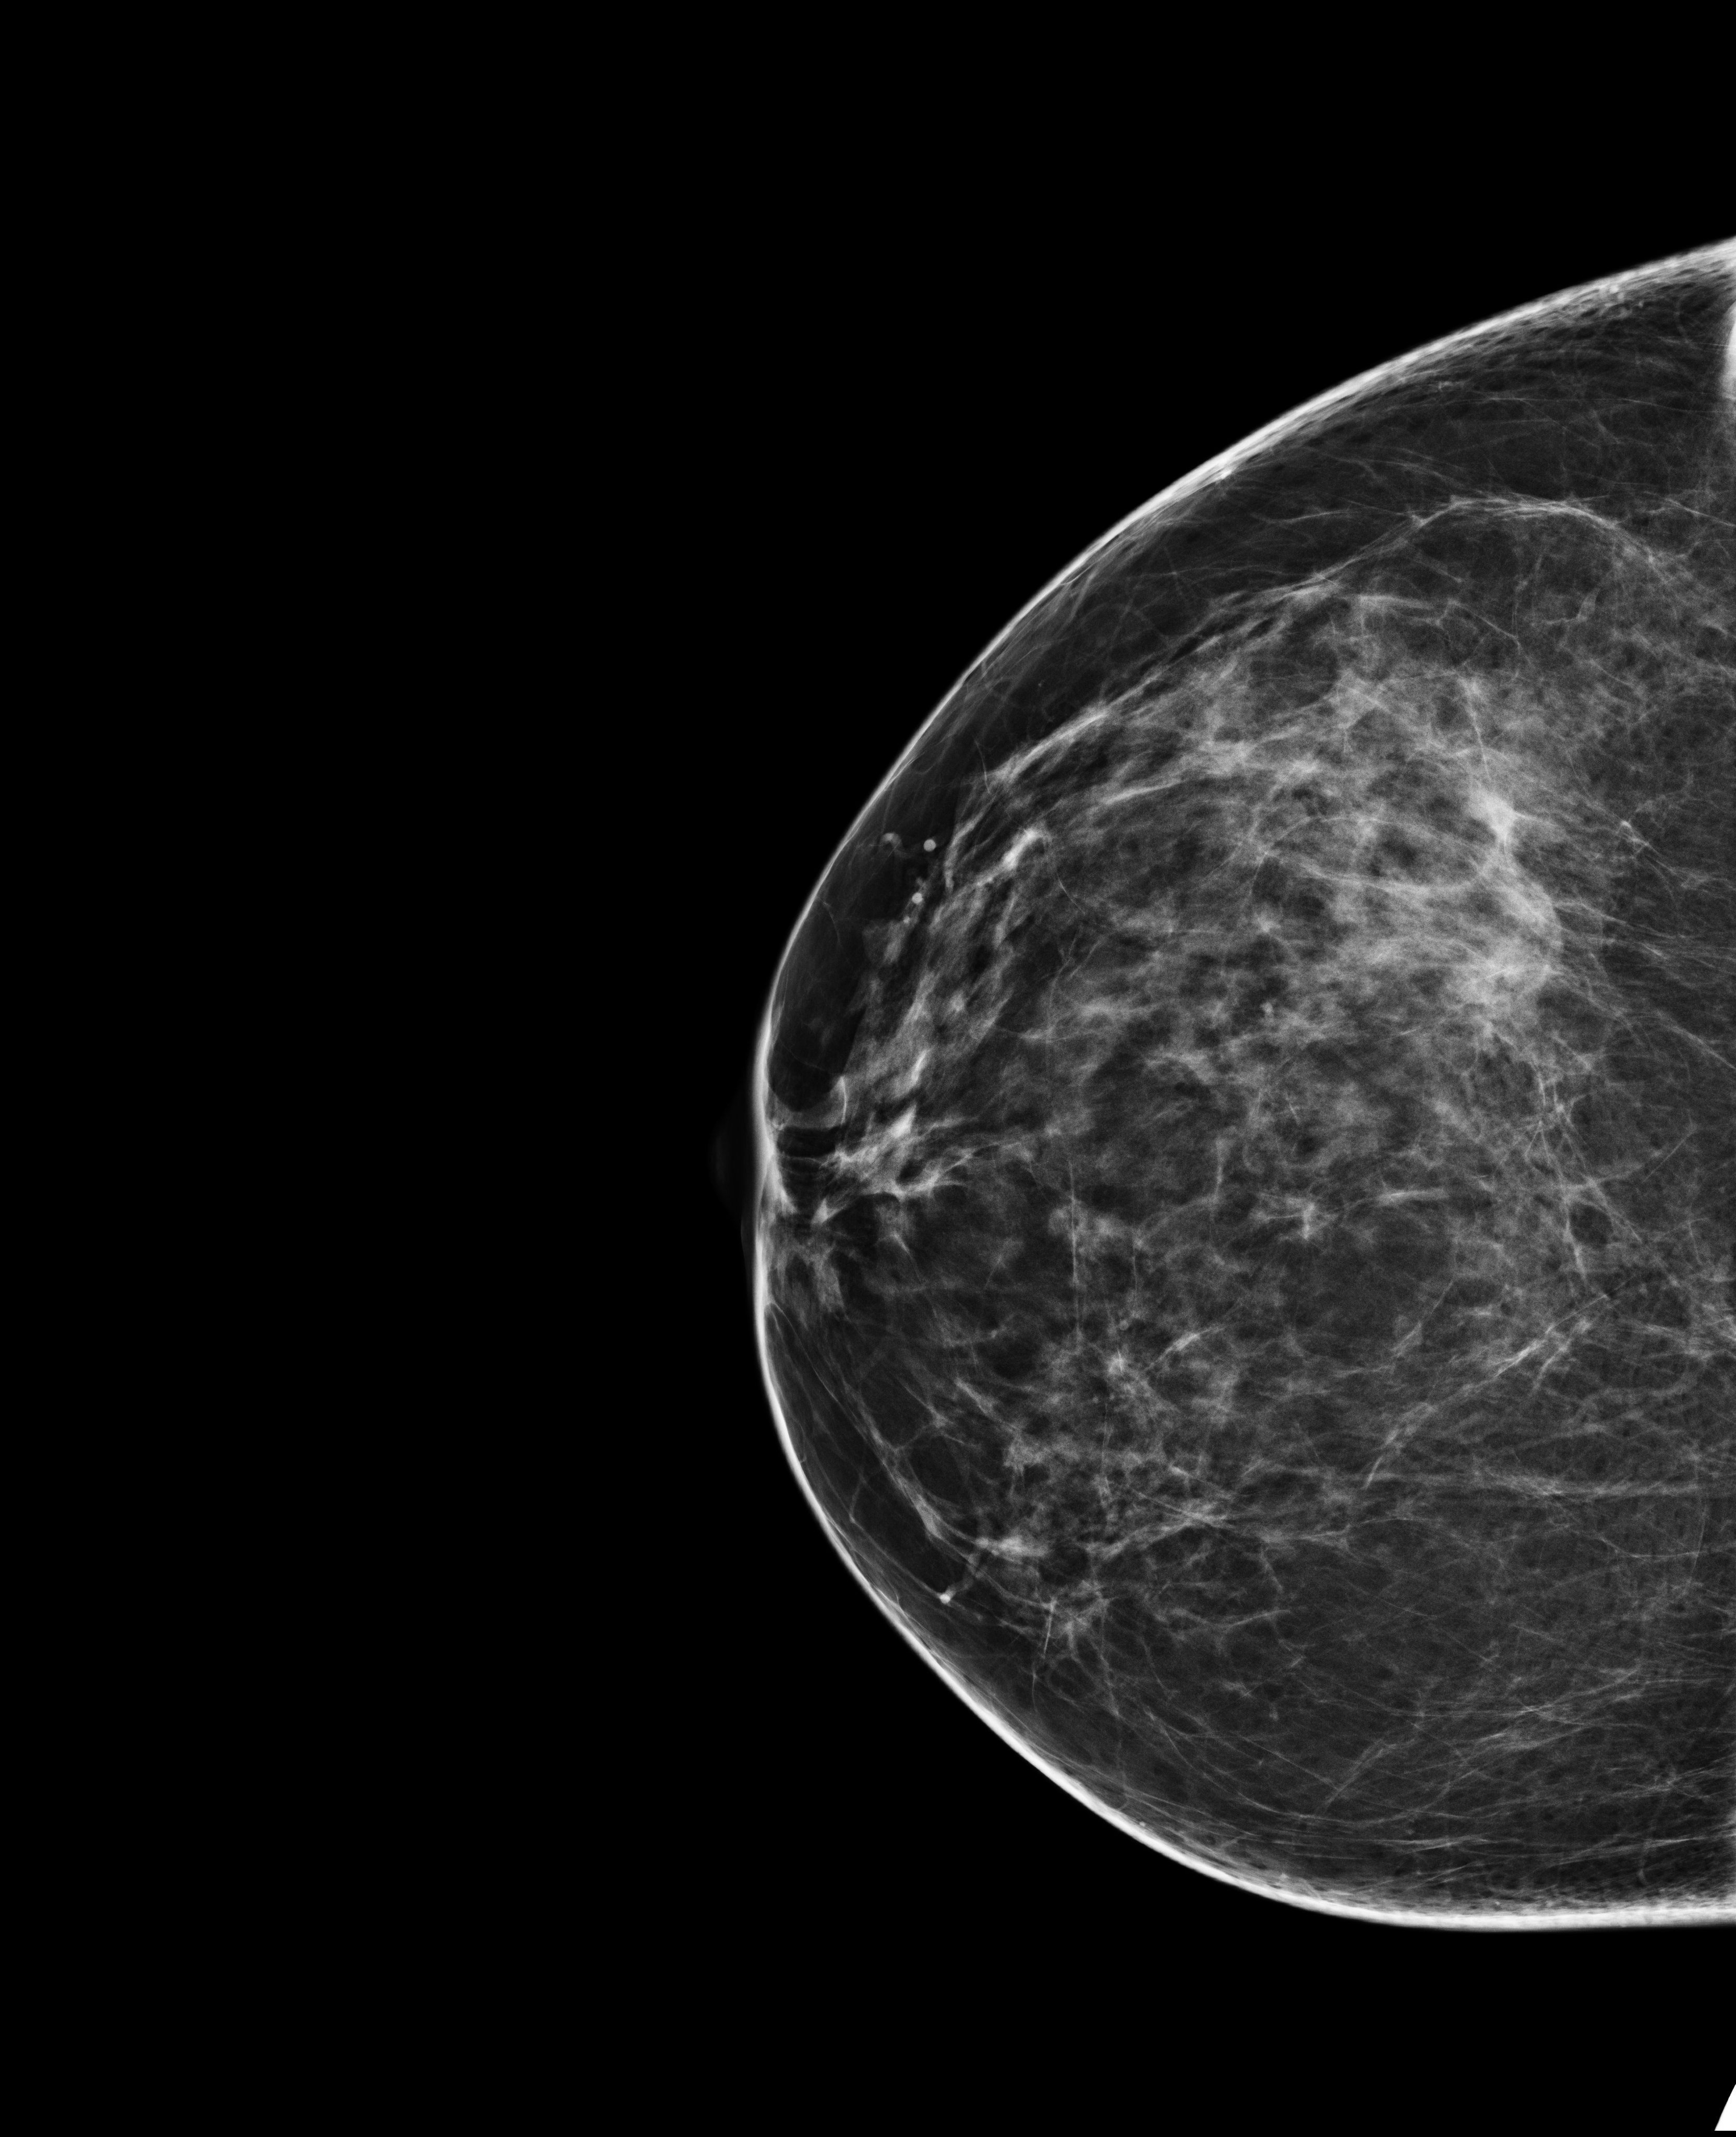
Screening examination; compressed breast thickness 74 mm; system: Selenia Dimensions. Patient: female, 50 years.
Image type: full-field digital mammogram. Breast: right. Projection: cranio-caudal projection. Breast density at the screening exam (both breasts): heterogeneously dense (BI-RADS density category c). Final BI-RADS category for the screening round (tomosynthesis exam, both breasts): category 1. Recall: no recall after this screen.